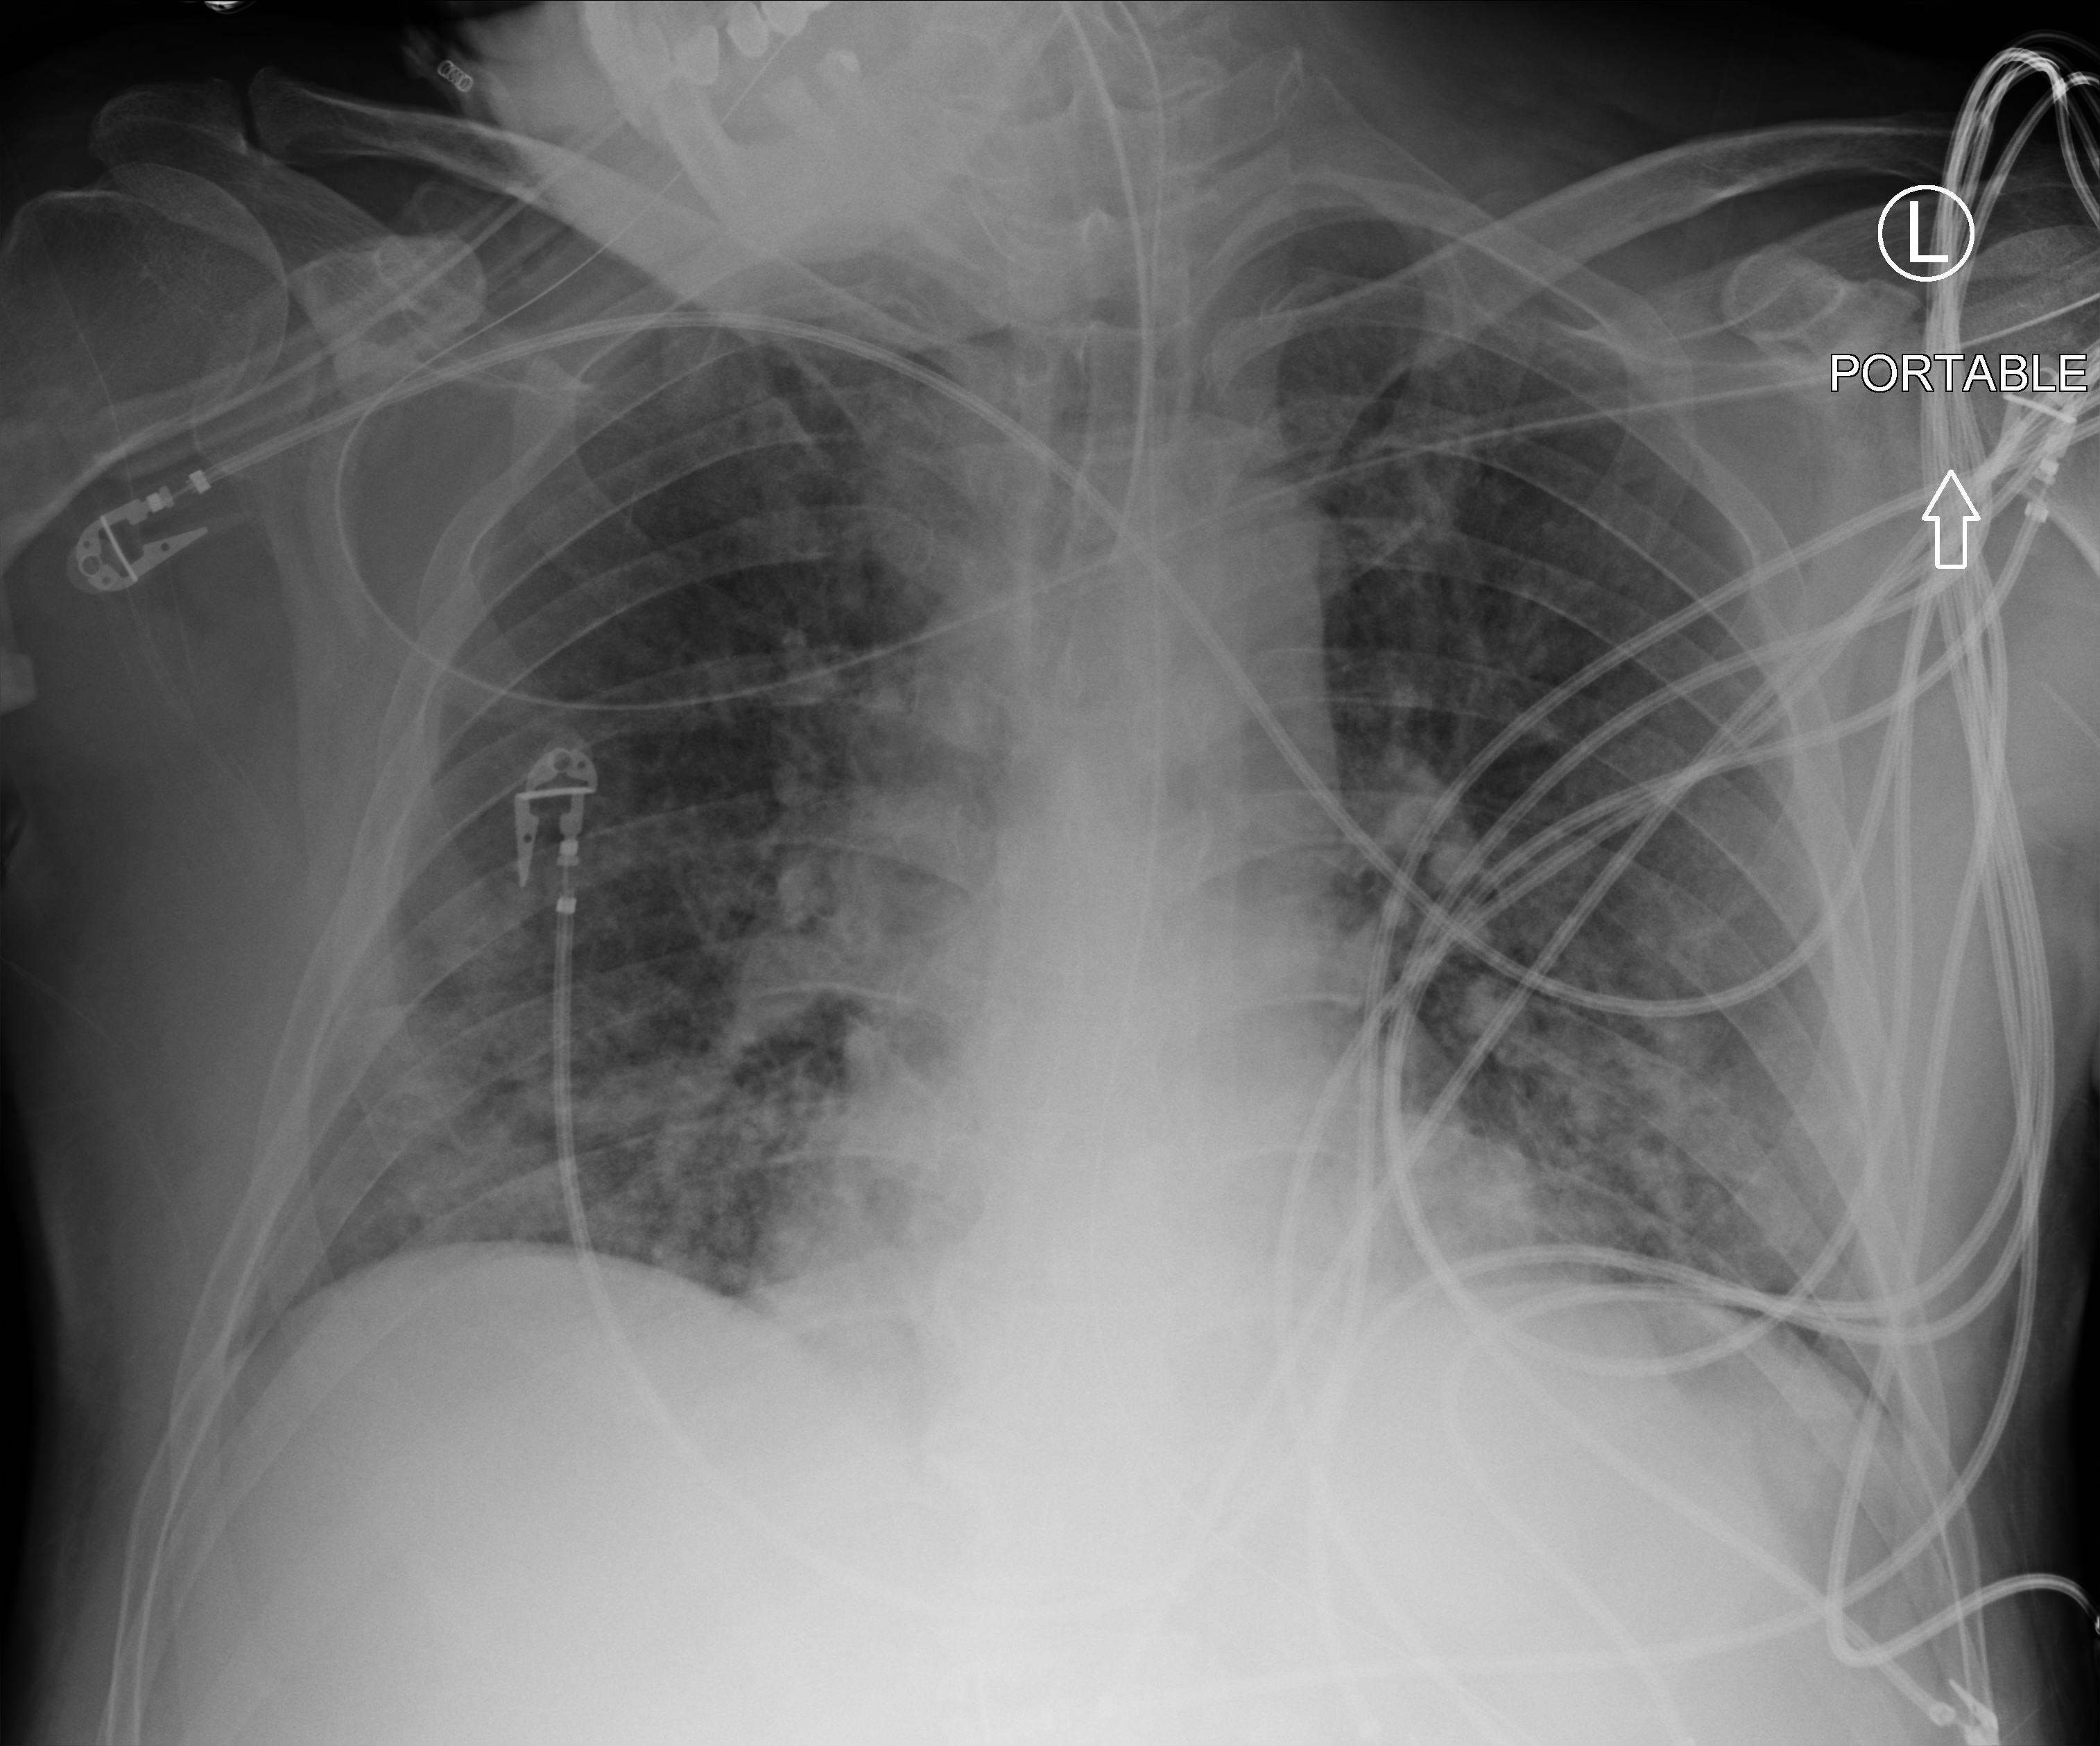
Chest X-ray (portable); anteroposterior (AP) projection. Patient hospitalised with COVID-19; male, aged 18–59 years.
From the hospital-stay record, not from the radiograph (when in the stay this image was taken is not recorded): admitted to intensive care during this hospital stay: no; chronic kidney disease (admission record): no.